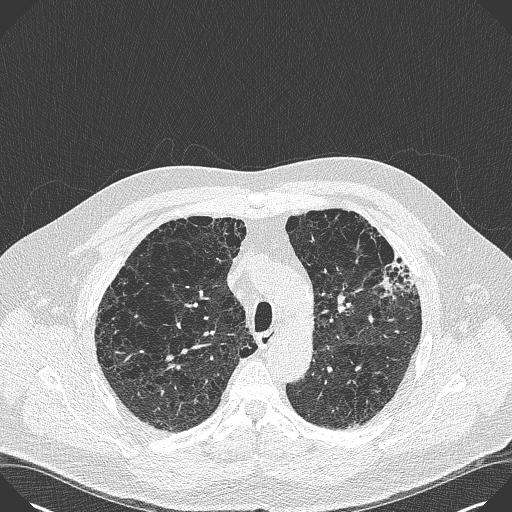
Axial slice from a low-dose chest CT screening exam. Baseline annual screen. Lung window (W 1500 / L -600 HU). 1 mm slice thickness. Male, age 59 years at enrolment.
Expert reader's lesion annotation, bounding box <373,249,429,300> (left, top, right, bottom; pixels). Screening reader's record for this exam: no non-calcified nodule ≥4 mm recorded. Official screen result: negative screen, minor abnormalities not suspicious for lung cancer. Participant outcome: lung cancer diagnosed 909 days after this screen — bronchiolo-alveolar carcinoma, mixed mucinous and non-mucinous, left upper lobe, stage IA (AJCC 6th edition), 20 mm at pathology.